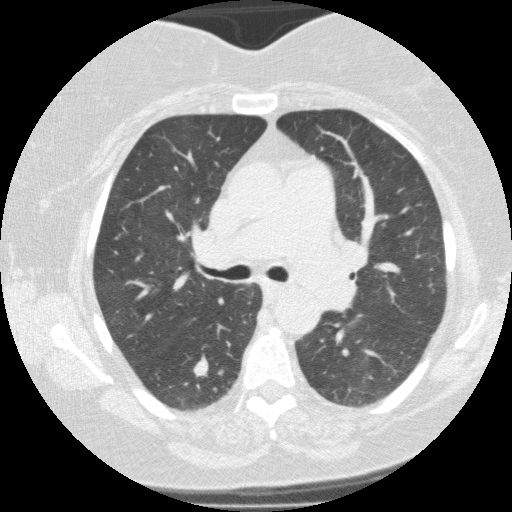
Low-dose screening chest CT, one axial slice. Slice 90 of 146 in the series (ordered by position). Reconstruction kernel FC01. 120 kVp. Lung window (W 1500 / L -600 HU). 2 mm slice thickness. 512 × 512 image matrix, field of view 330 × 330 mm.
Outlined on this slice (outlined manually by an expert reader):
- lesion 3 (nodule, lower lobe of right lung): bounding box [x1, y1, x2, y2] px = [194, 358, 210, 378]